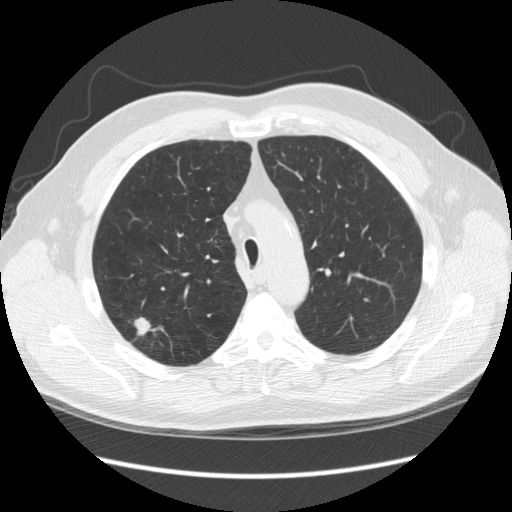
Low-dose screening chest CT, one axial slice. Position 185 of 248 along the scan axis. Reconstruction kernel STANDARD. Lung window (W 1500 / L -600 HU). 2.5 mm slice thickness. 512 × 512 image matrix, field of view 380 × 380 mm.
Outlined on this slice (expert manual segmentation):
- lesion 1 (tumor, upper lobe of right lung): bounding box [x1, y1, x2, y2] px = [134, 317, 151, 336]